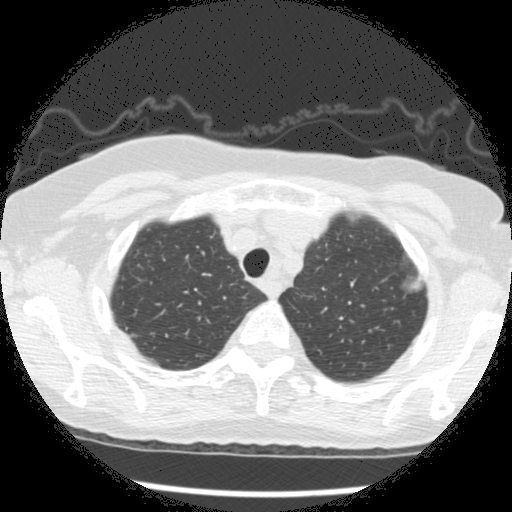
Low-dose screening chest CT, one axial slice. Slice 233 of 266 in the series (ordered by position). 120 kVp. Lung window (W 1500 / L -600 HU). 2.5 mm slice thickness. 512 × 512 image matrix, field of view 320 × 320 mm.
Structures marked on this image (manually delineated by an expert):
- lesion 1 (tumor, upper lobe of left lung): box from (x=409, y=279) to (x=422, y=290) px